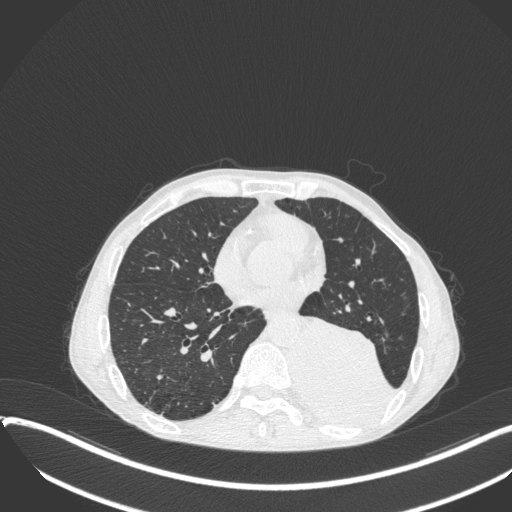
Chest CT, one axial slice; slice 146 of 400 in the series (ordered by position); reconstruction kernel B31f; 120 kVp; lung window (W 1500 / L -600 HU); 1 mm slice thickness; 512 × 512 image matrix, field of view 400 × 400 mm. Male patient, age 57 years. Case-level facts recorded for this patient, not image findings: clinical TNM (as recorded): T4 N0 M0.
Outlined on this slice (rectangle marked by the reading radiologist):
- lung tumour (recorded histology: squamous cell carcinoma): bounding box <288,309,394,432> (left, top, right, bottom; pixels)